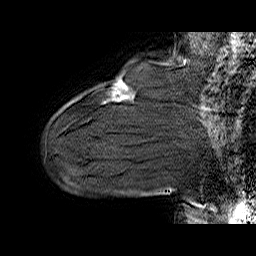
Breast MRI (dynamic contrast-enhanced), one sagittal slice; slice 12 of 60 in the series (ordered by position); dynamic contrast-enhanced series, time point 2 of 6 at this slice position (early post-contrast); 1.5 T; TE 6.4 ms, TR 32.9 ms; 256 × 256 image matrix, field of view 200 × 200 mm. Female patient. Case-level facts recorded for this patient, not image findings: setting: breast cancer imaged before/during neoadjuvant chemotherapy; receptor status: HER2-positive.
Outlined on this slice (semi-automatically segmented with operator editing):
- analysis volume of interest (the breast-tissue region the enhancement analysis was run in; not a lesion): bounding box <110,76,134,102> (left, top, right, bottom; pixels)
- tumour enhancement mask (voxels above the 100 % enhancement threshold inside the analysis volume of interest): <117,83,127,94>